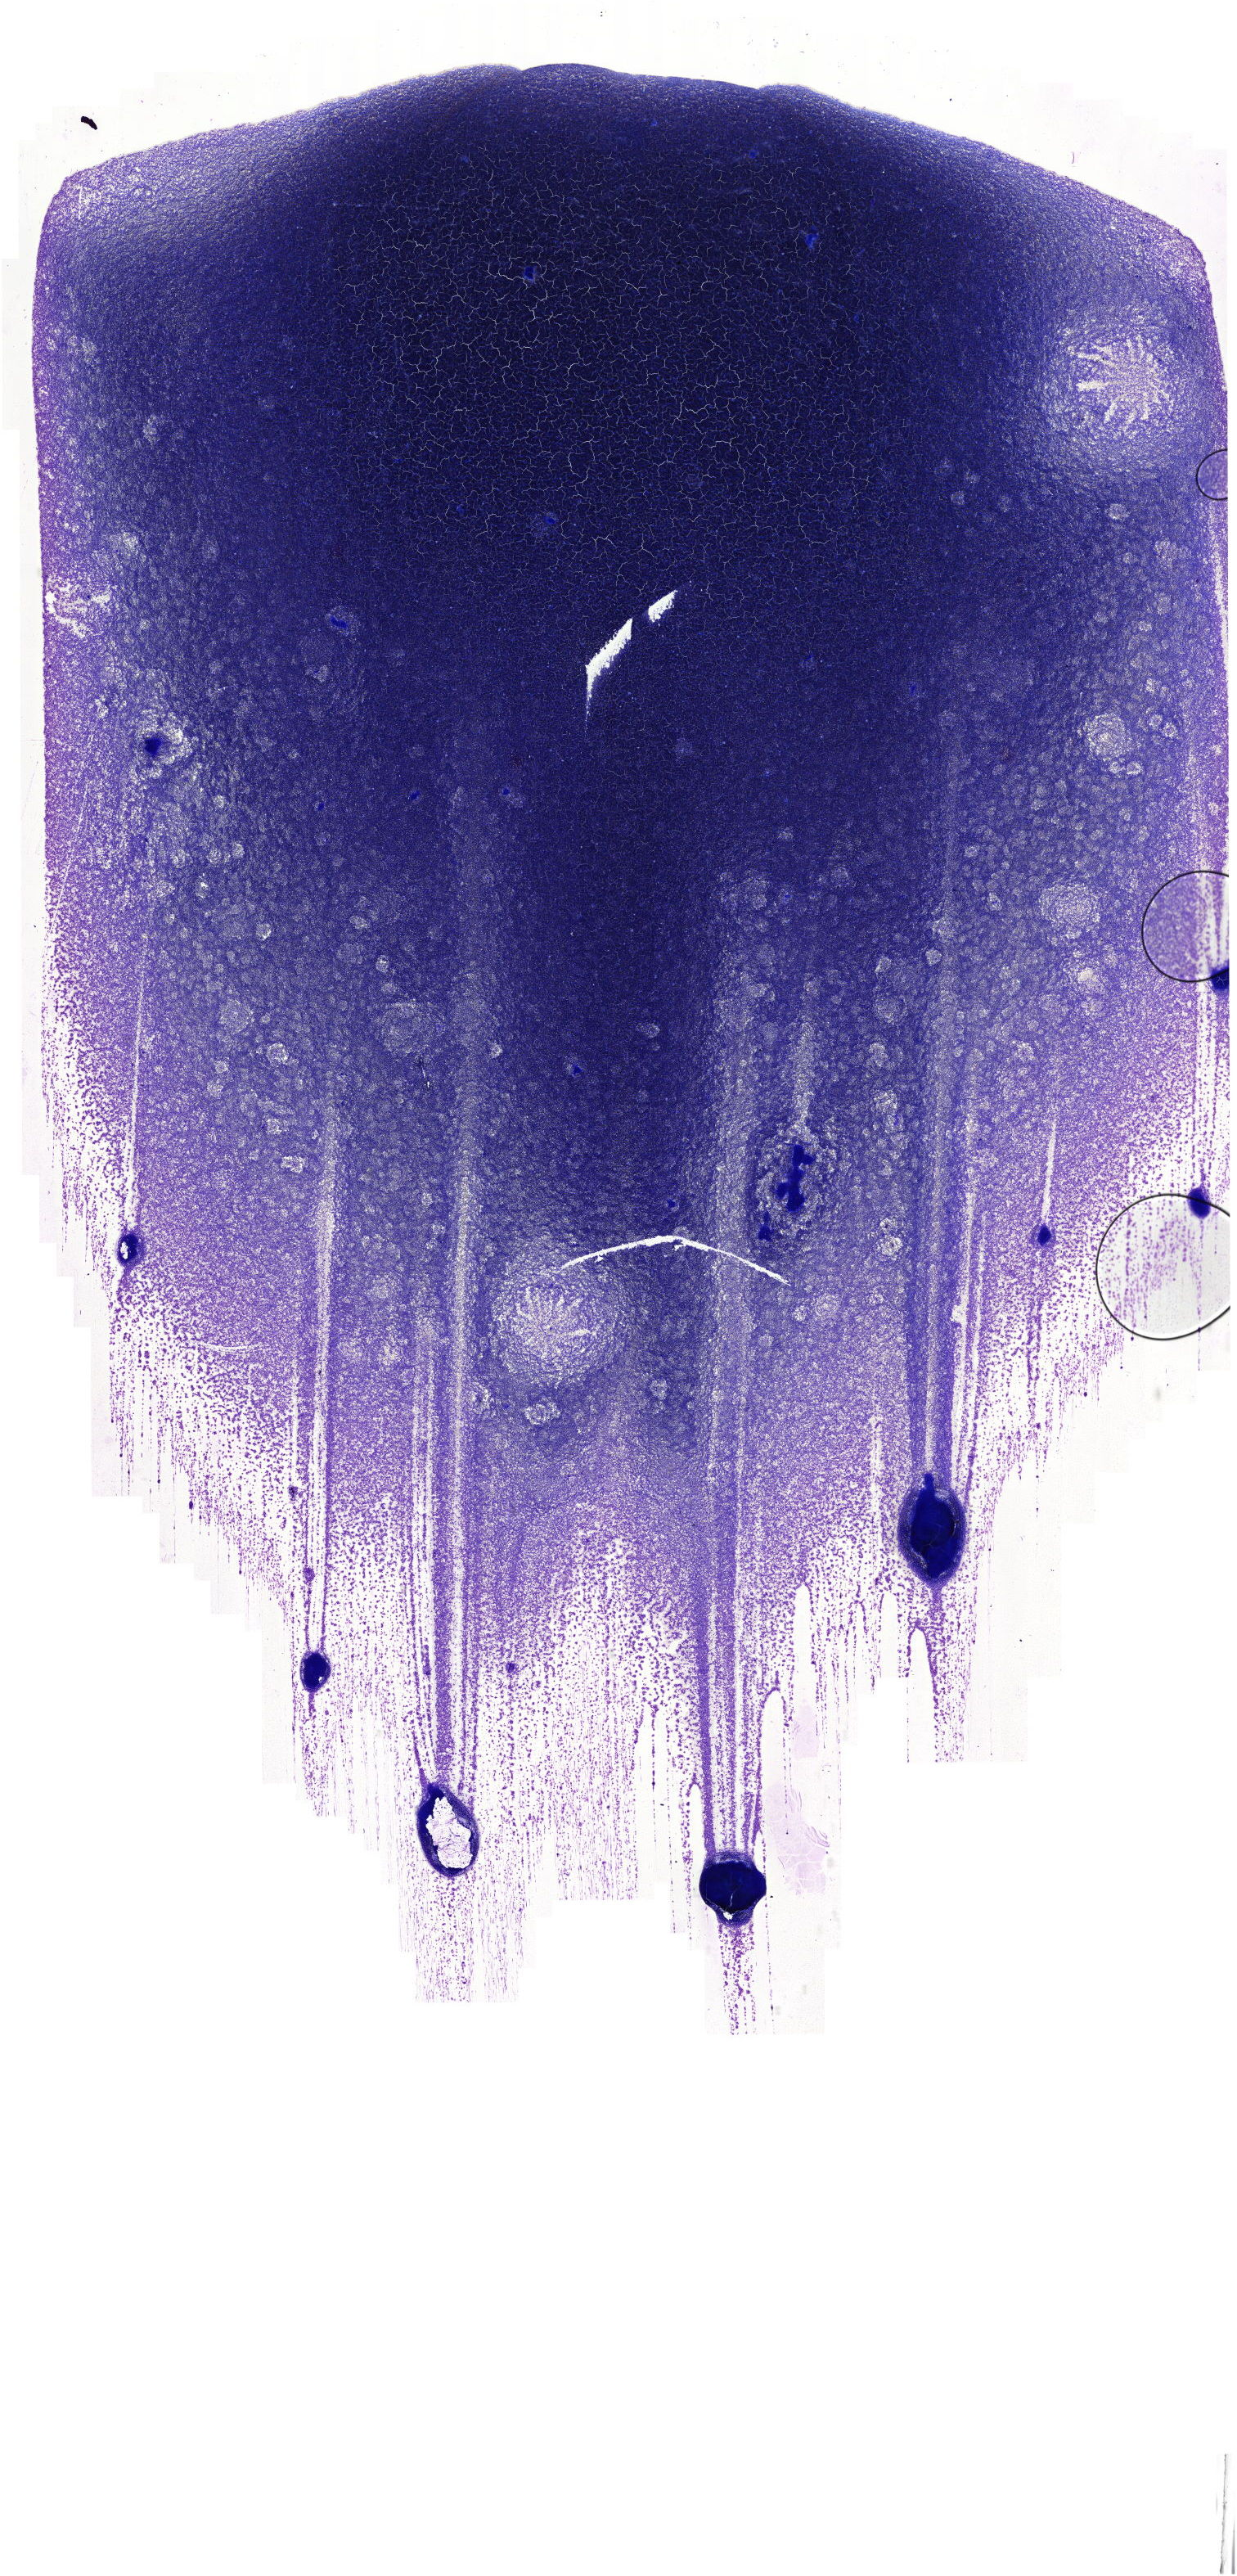
Whole-slide image of a May-Grünwald–Giemsa-stained bone marrow aspirate smear — shown as a low-resolution overview of the whole scanned area (about 18.8 x 39.2 mm). Patient sex: male.
Diagnosis: Chronic Phase Chronic Myeloid Leukemia, BCR-ABL1 Positive.